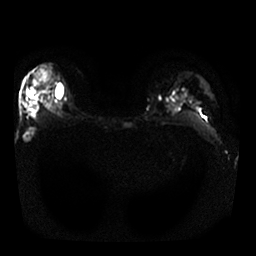
Breast MRI, one axial slice. Slice 20 of 30 in the series (ordered by position). Diffusion-weighted series; image 2 of 4 stored at this slice position (different b-values; order by instance number). 1.5 T. 4 mm slice thickness. 256 × 256 image matrix, field of view 340 × 340 mm. Female patient.
Annotated regions visible in this slice (outlined manually by an expert reader):
- tumour on diffusion-weighted imaging: bounding box (x1, y1, x2, y2) in pixels: (39, 69, 50, 83)